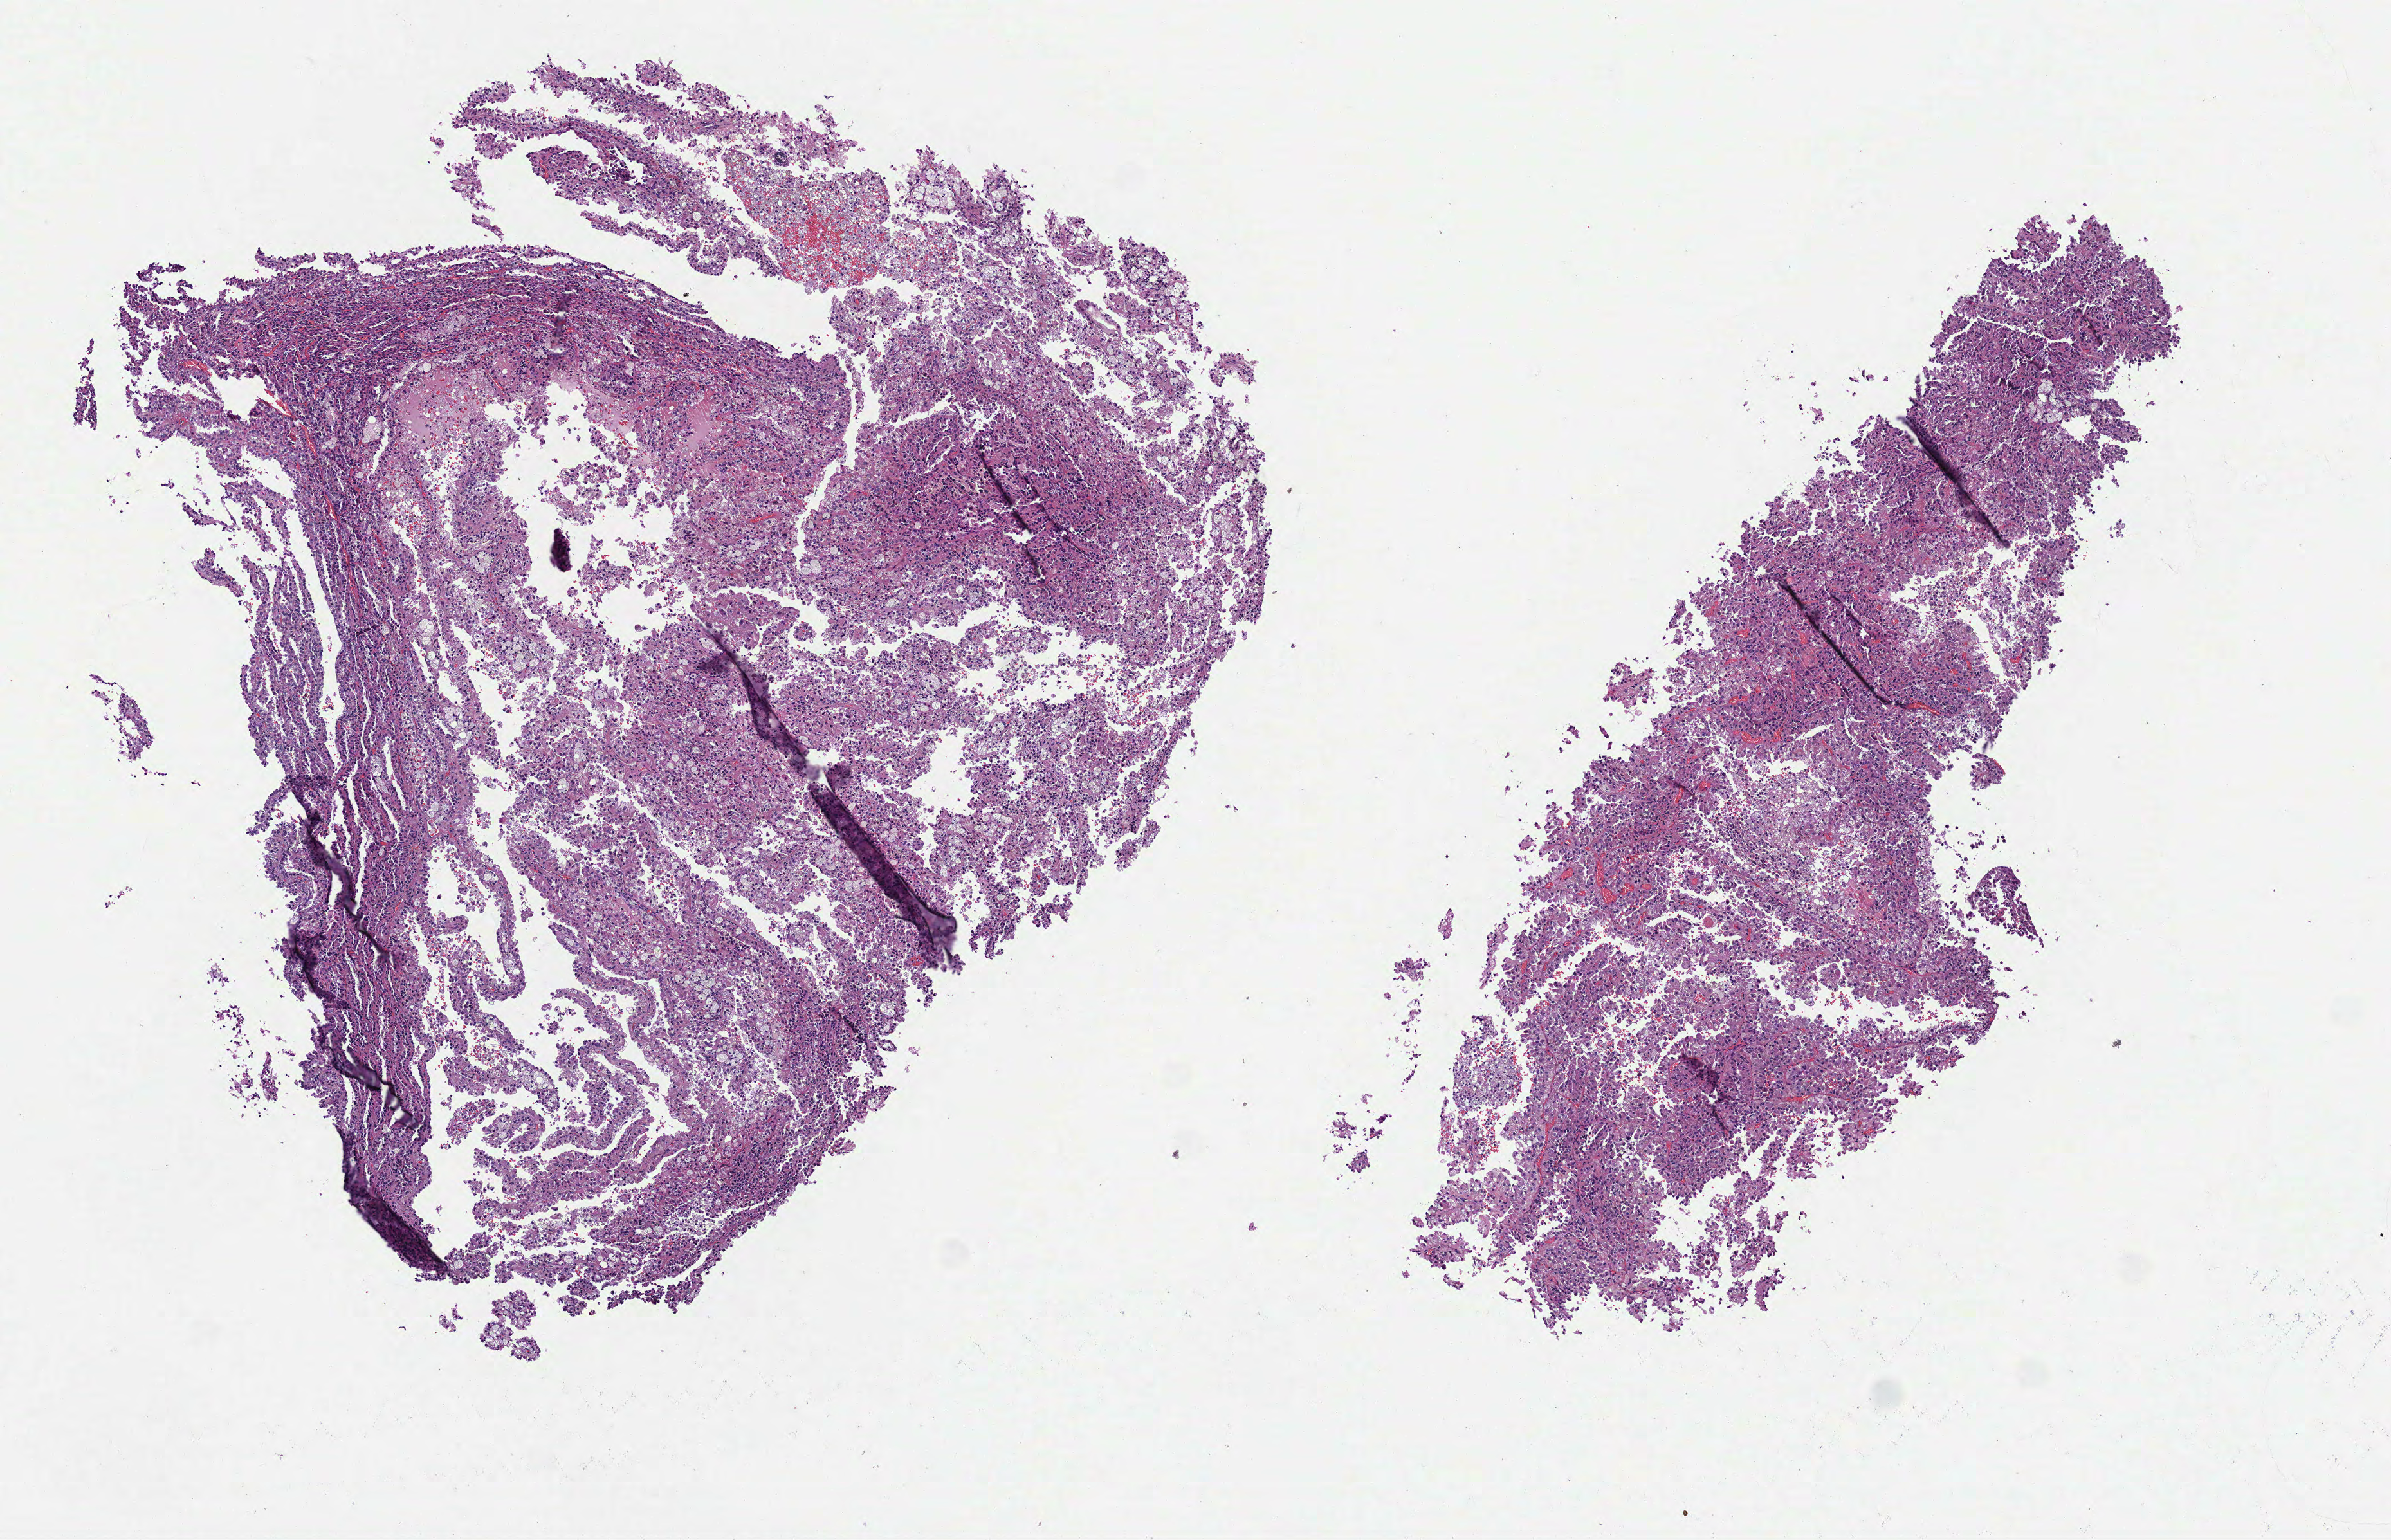
Whole-slide histology image, Hematoxylin and eosin (H&E) stained — whole scanned area (about 7.5 x 4.8 mm, slide scanned at 40x) shown as a low-resolution overview, FFPE section, sample: primary tumour, kidney. Patient: male, age at initial diagnosis 58 years.
Pathologic diagnosis: Papillary adenocarcinoma, NOS. AJCC pathologic stage: III (7th edition).